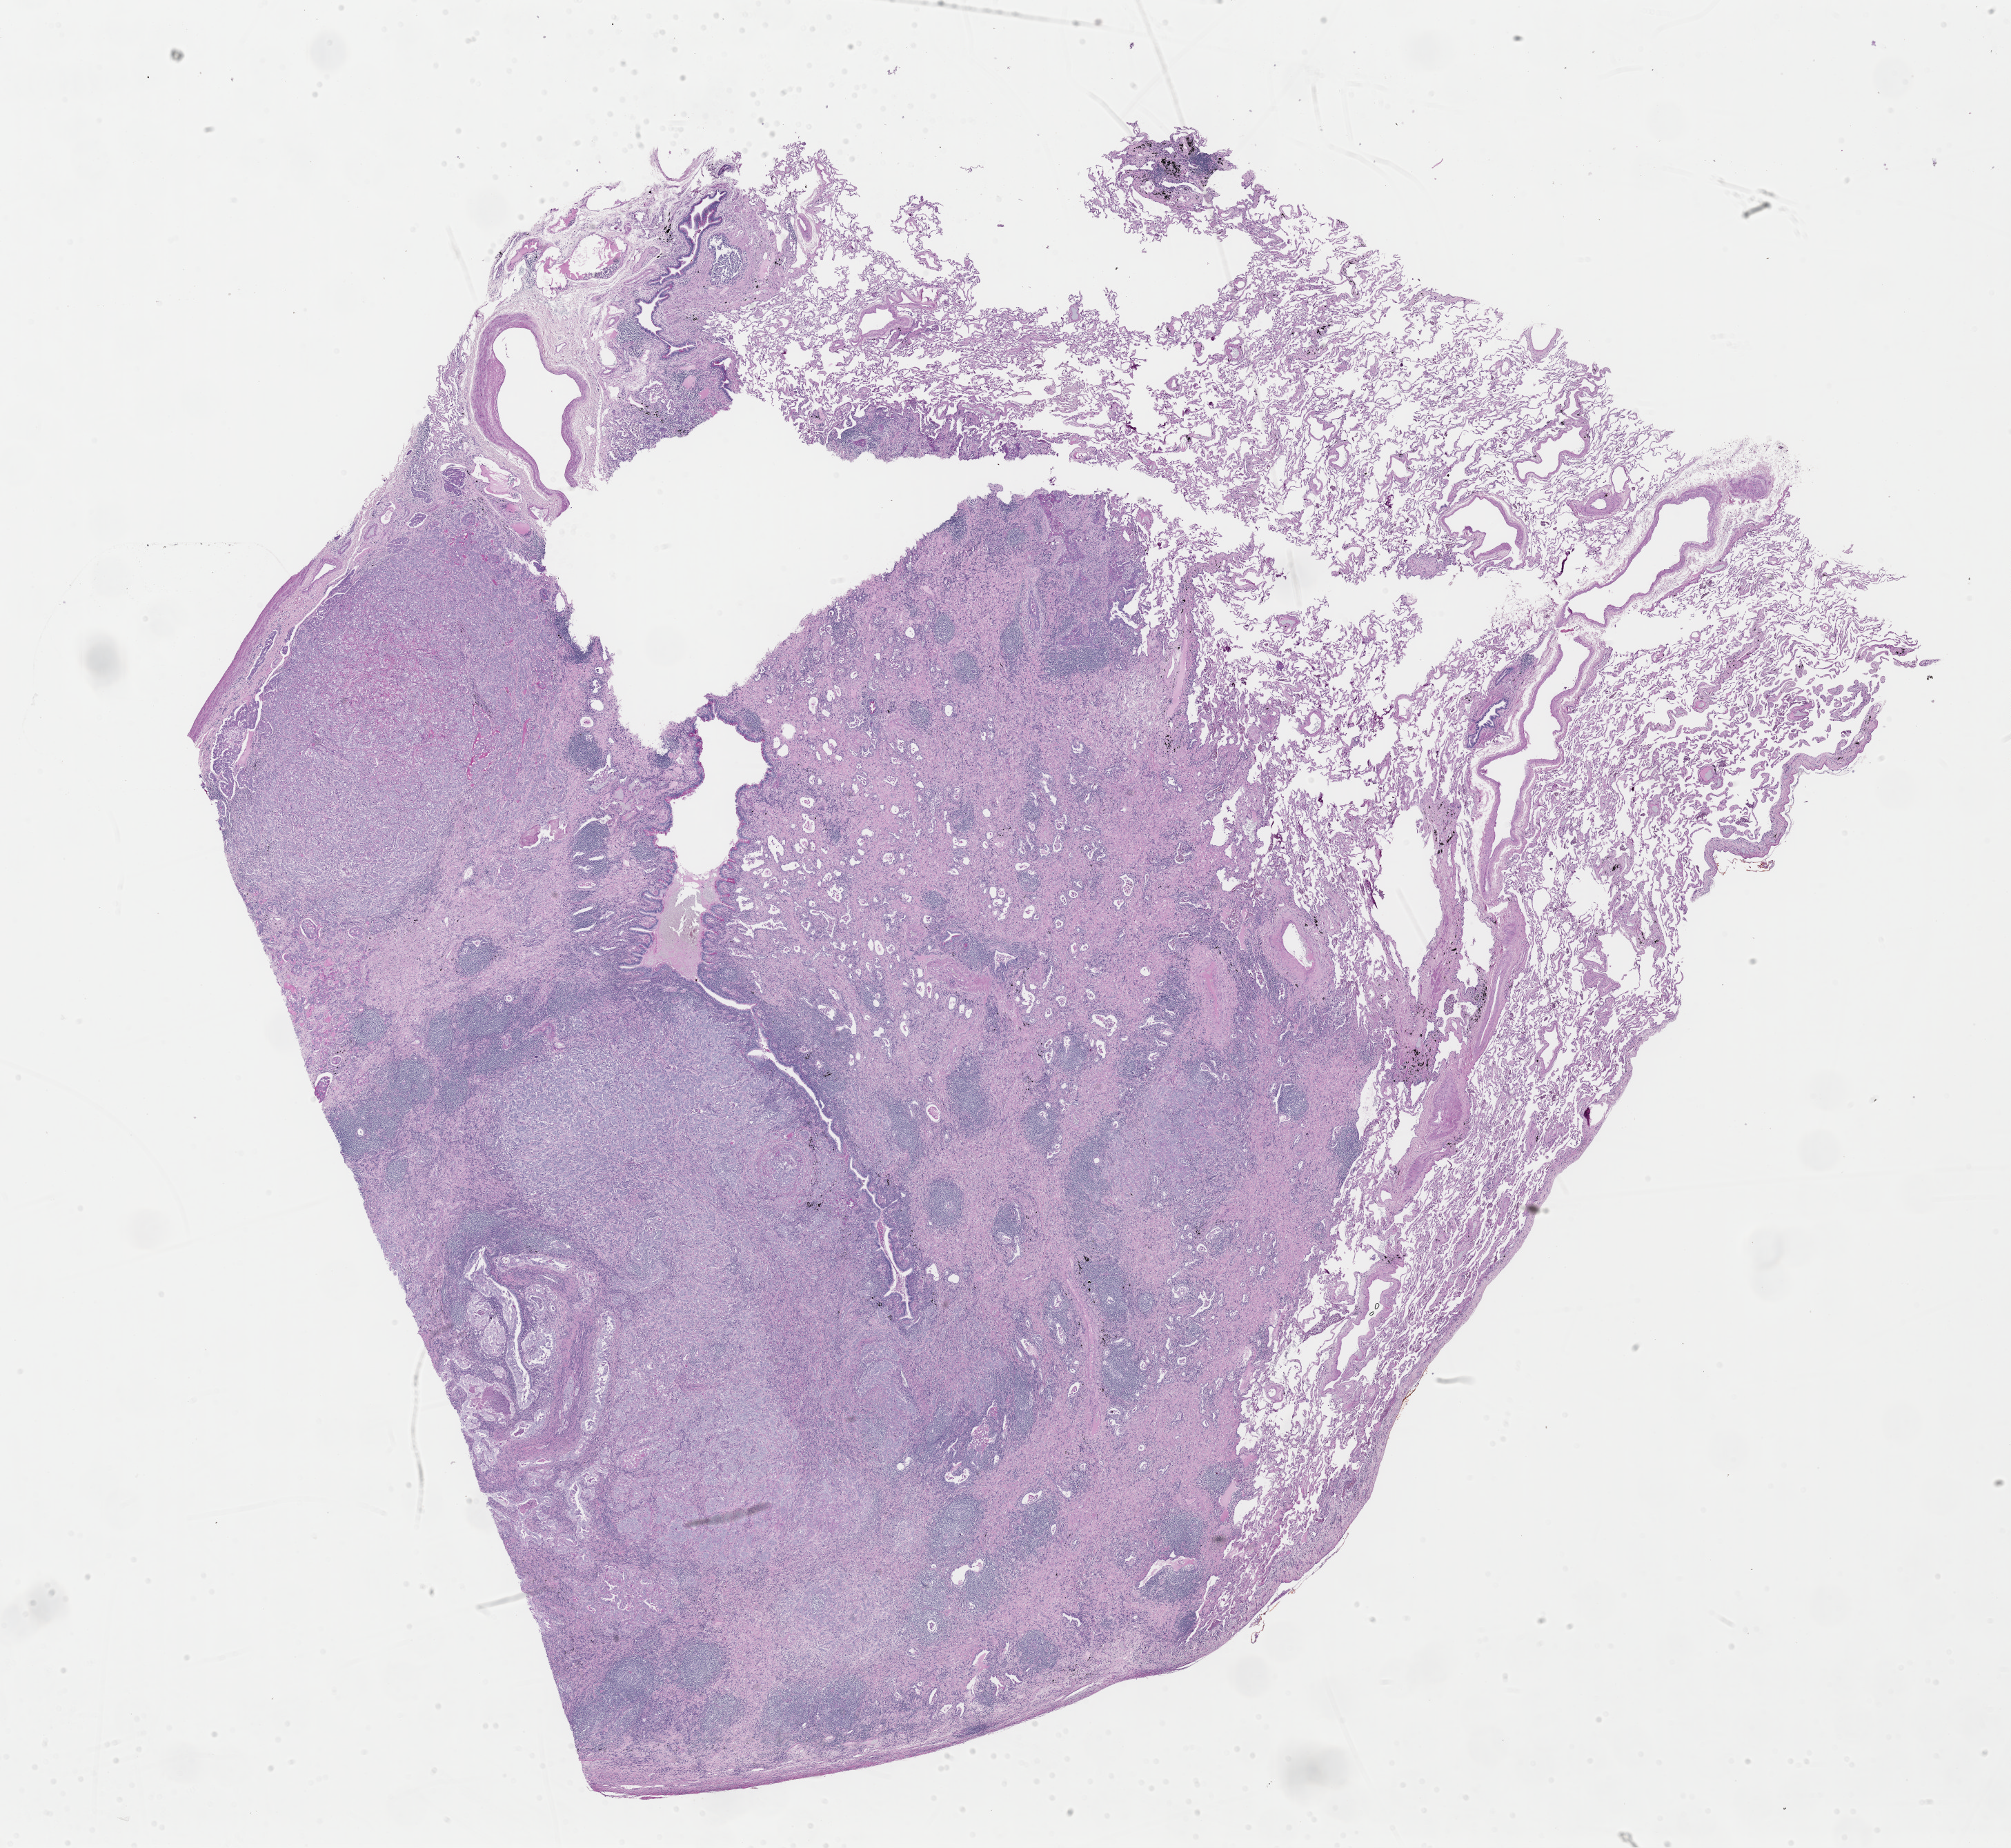
Whole-slide histology image, H&E-stained, whole scanned area (about 23.0 x 21.2 mm) shown as a low-resolution overview. Formalin-fixed paraffin-embedded (FFPE) diagnostic section. Lung, primary tumour sample. Male patient; age at initial diagnosis 85 years.
AJCC pathologic stage: IB (6th edition). Histologic diagnosis: Adenocarcinoma with mixed subtypes (upper lobe, lung).